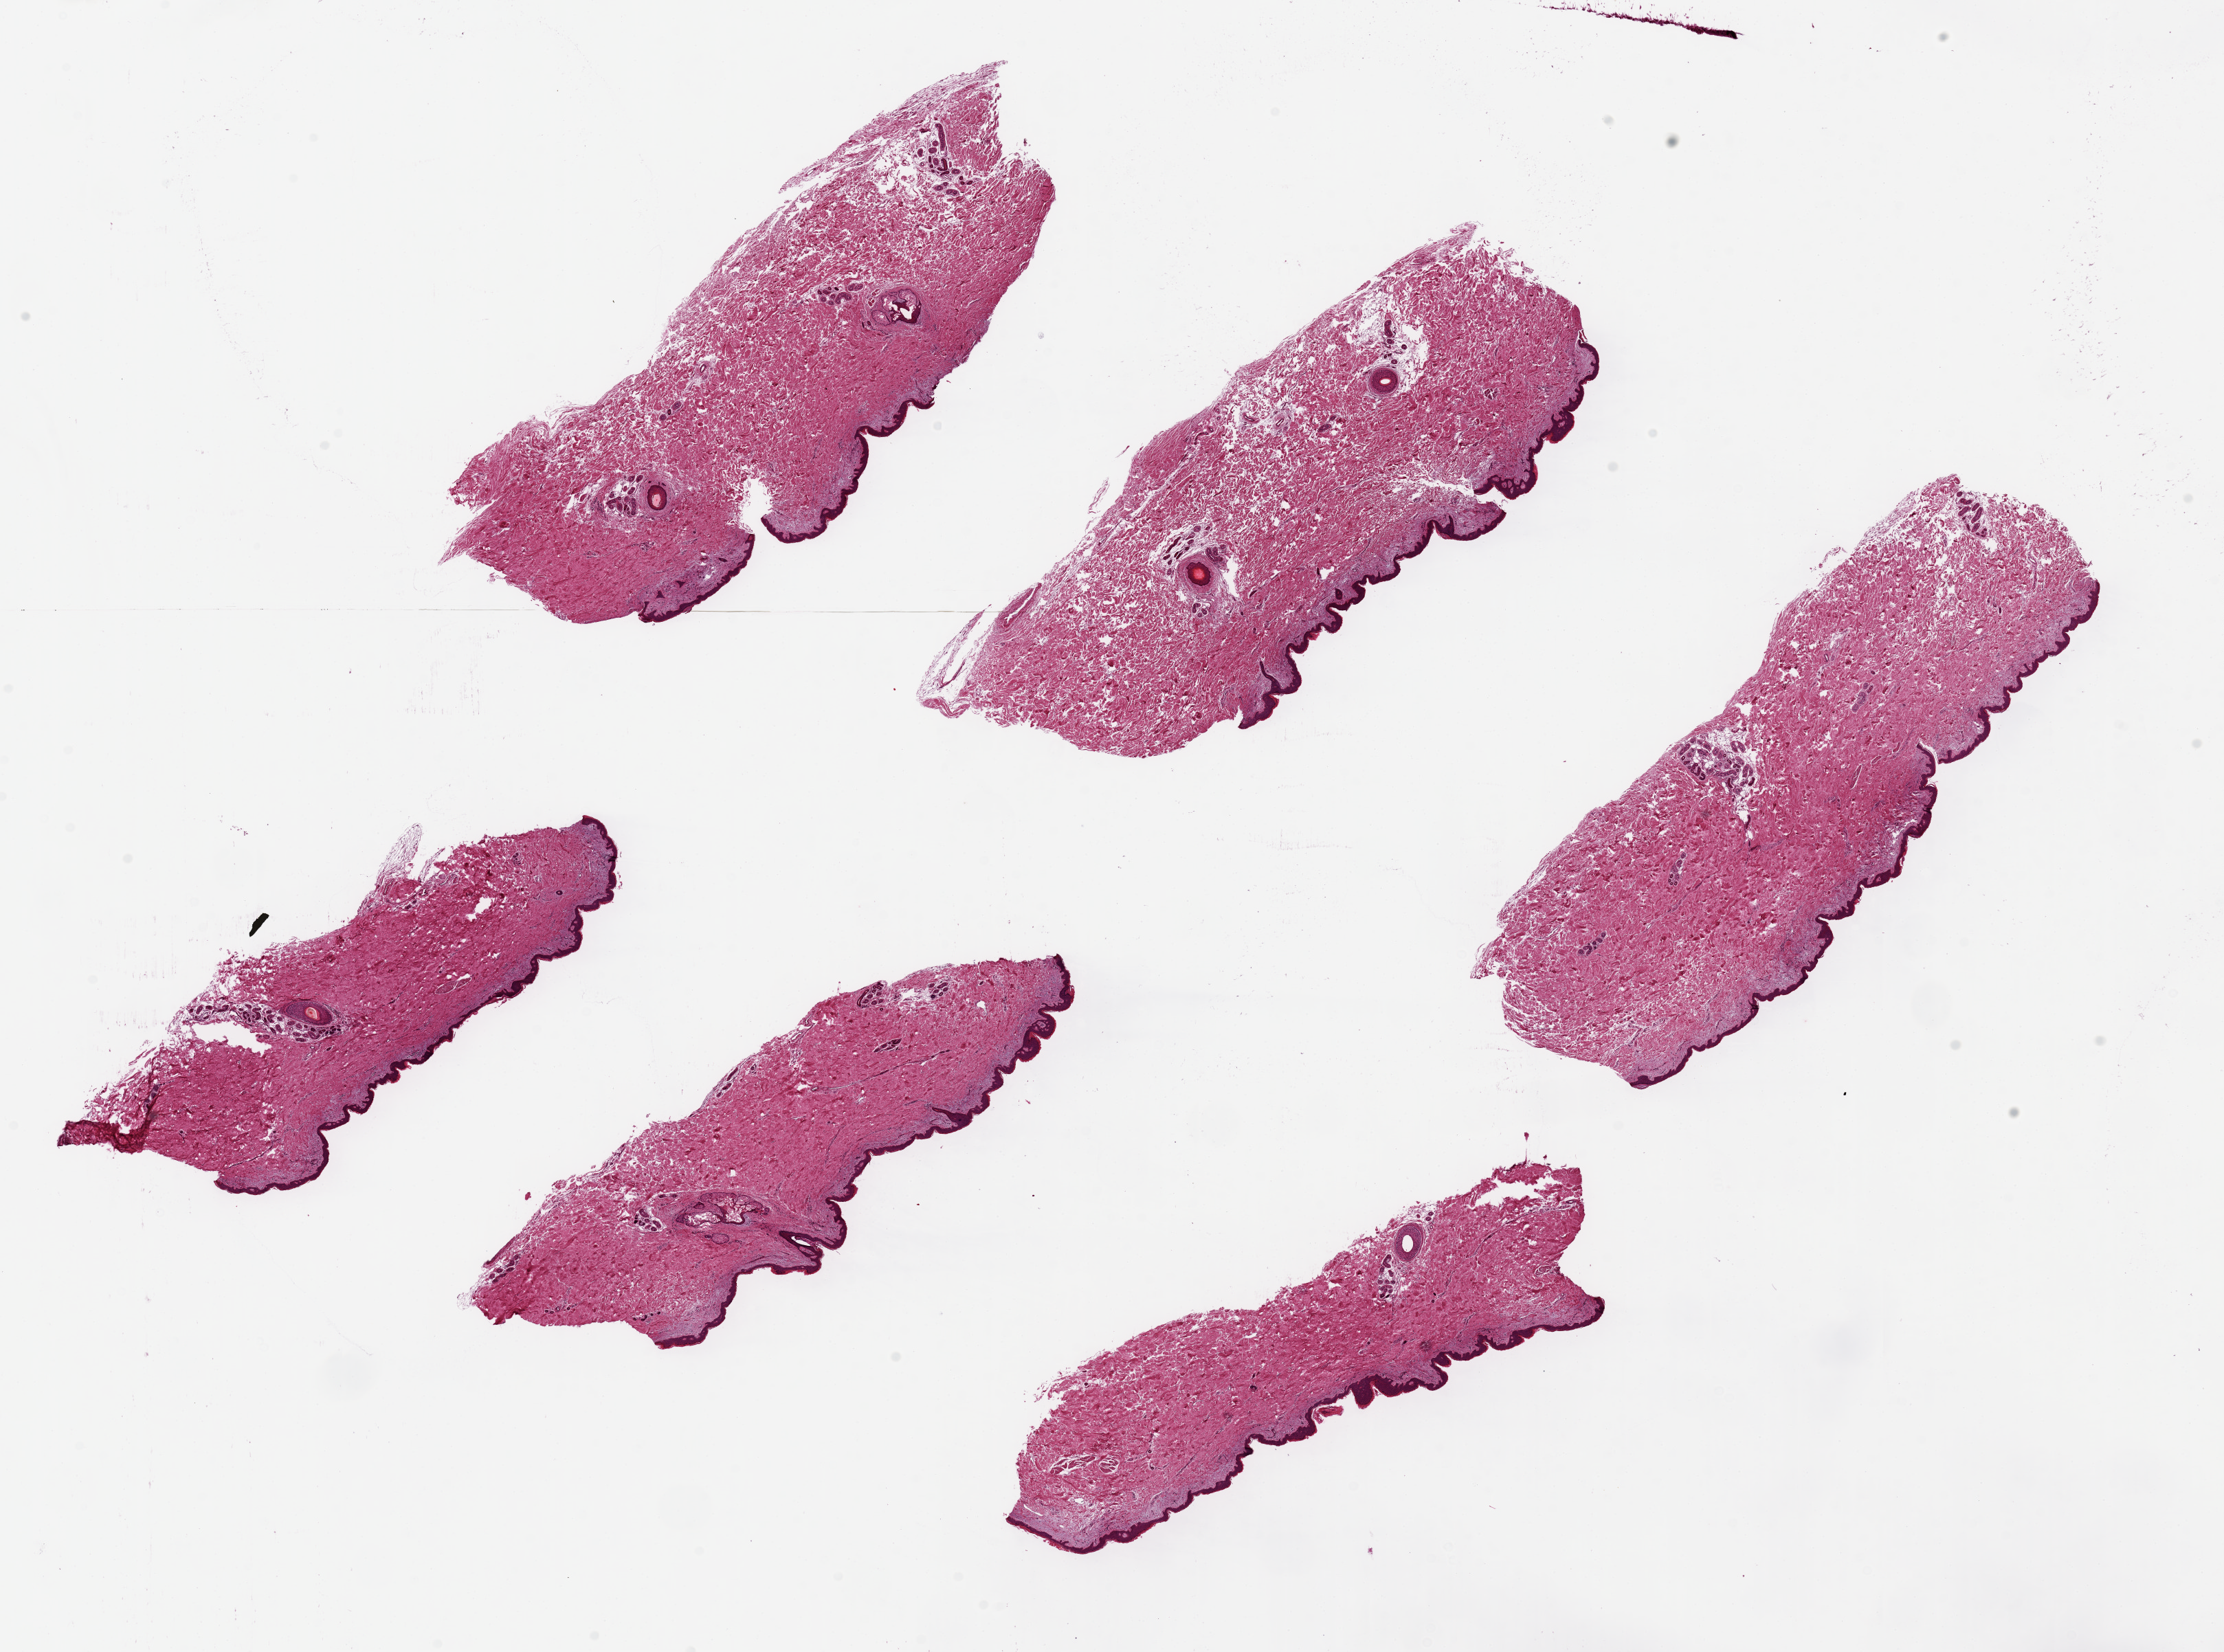
Digitized haematoxylin and eosin-stained section — a low-resolution overview of the entire scanned area, about 25.6 x 19.0 mm (from a 20x scan), PAXgene-fixed, paraffin-embedded tissue, section of skin of suprapubic region (target tissue), donor tissue sample. Male donor.
Review note (as recorded): 6 pieces, up to 9x3mm; well dissected without subcutaneous adipose.